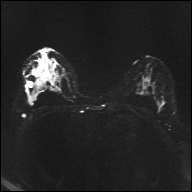
Breast MRI, one axial slice. Diffusion-weighted series; image 2 of 4 stored at this slice position (different b-values; order by instance number). 1.5 T. 192 × 192 image matrix, field of view 360 × 360 mm. Female patient.
Outlined on this slice (expert manual segmentation):
- tumour on diffusion-weighted imaging: box from (x=39, y=65) to (x=46, y=73) px